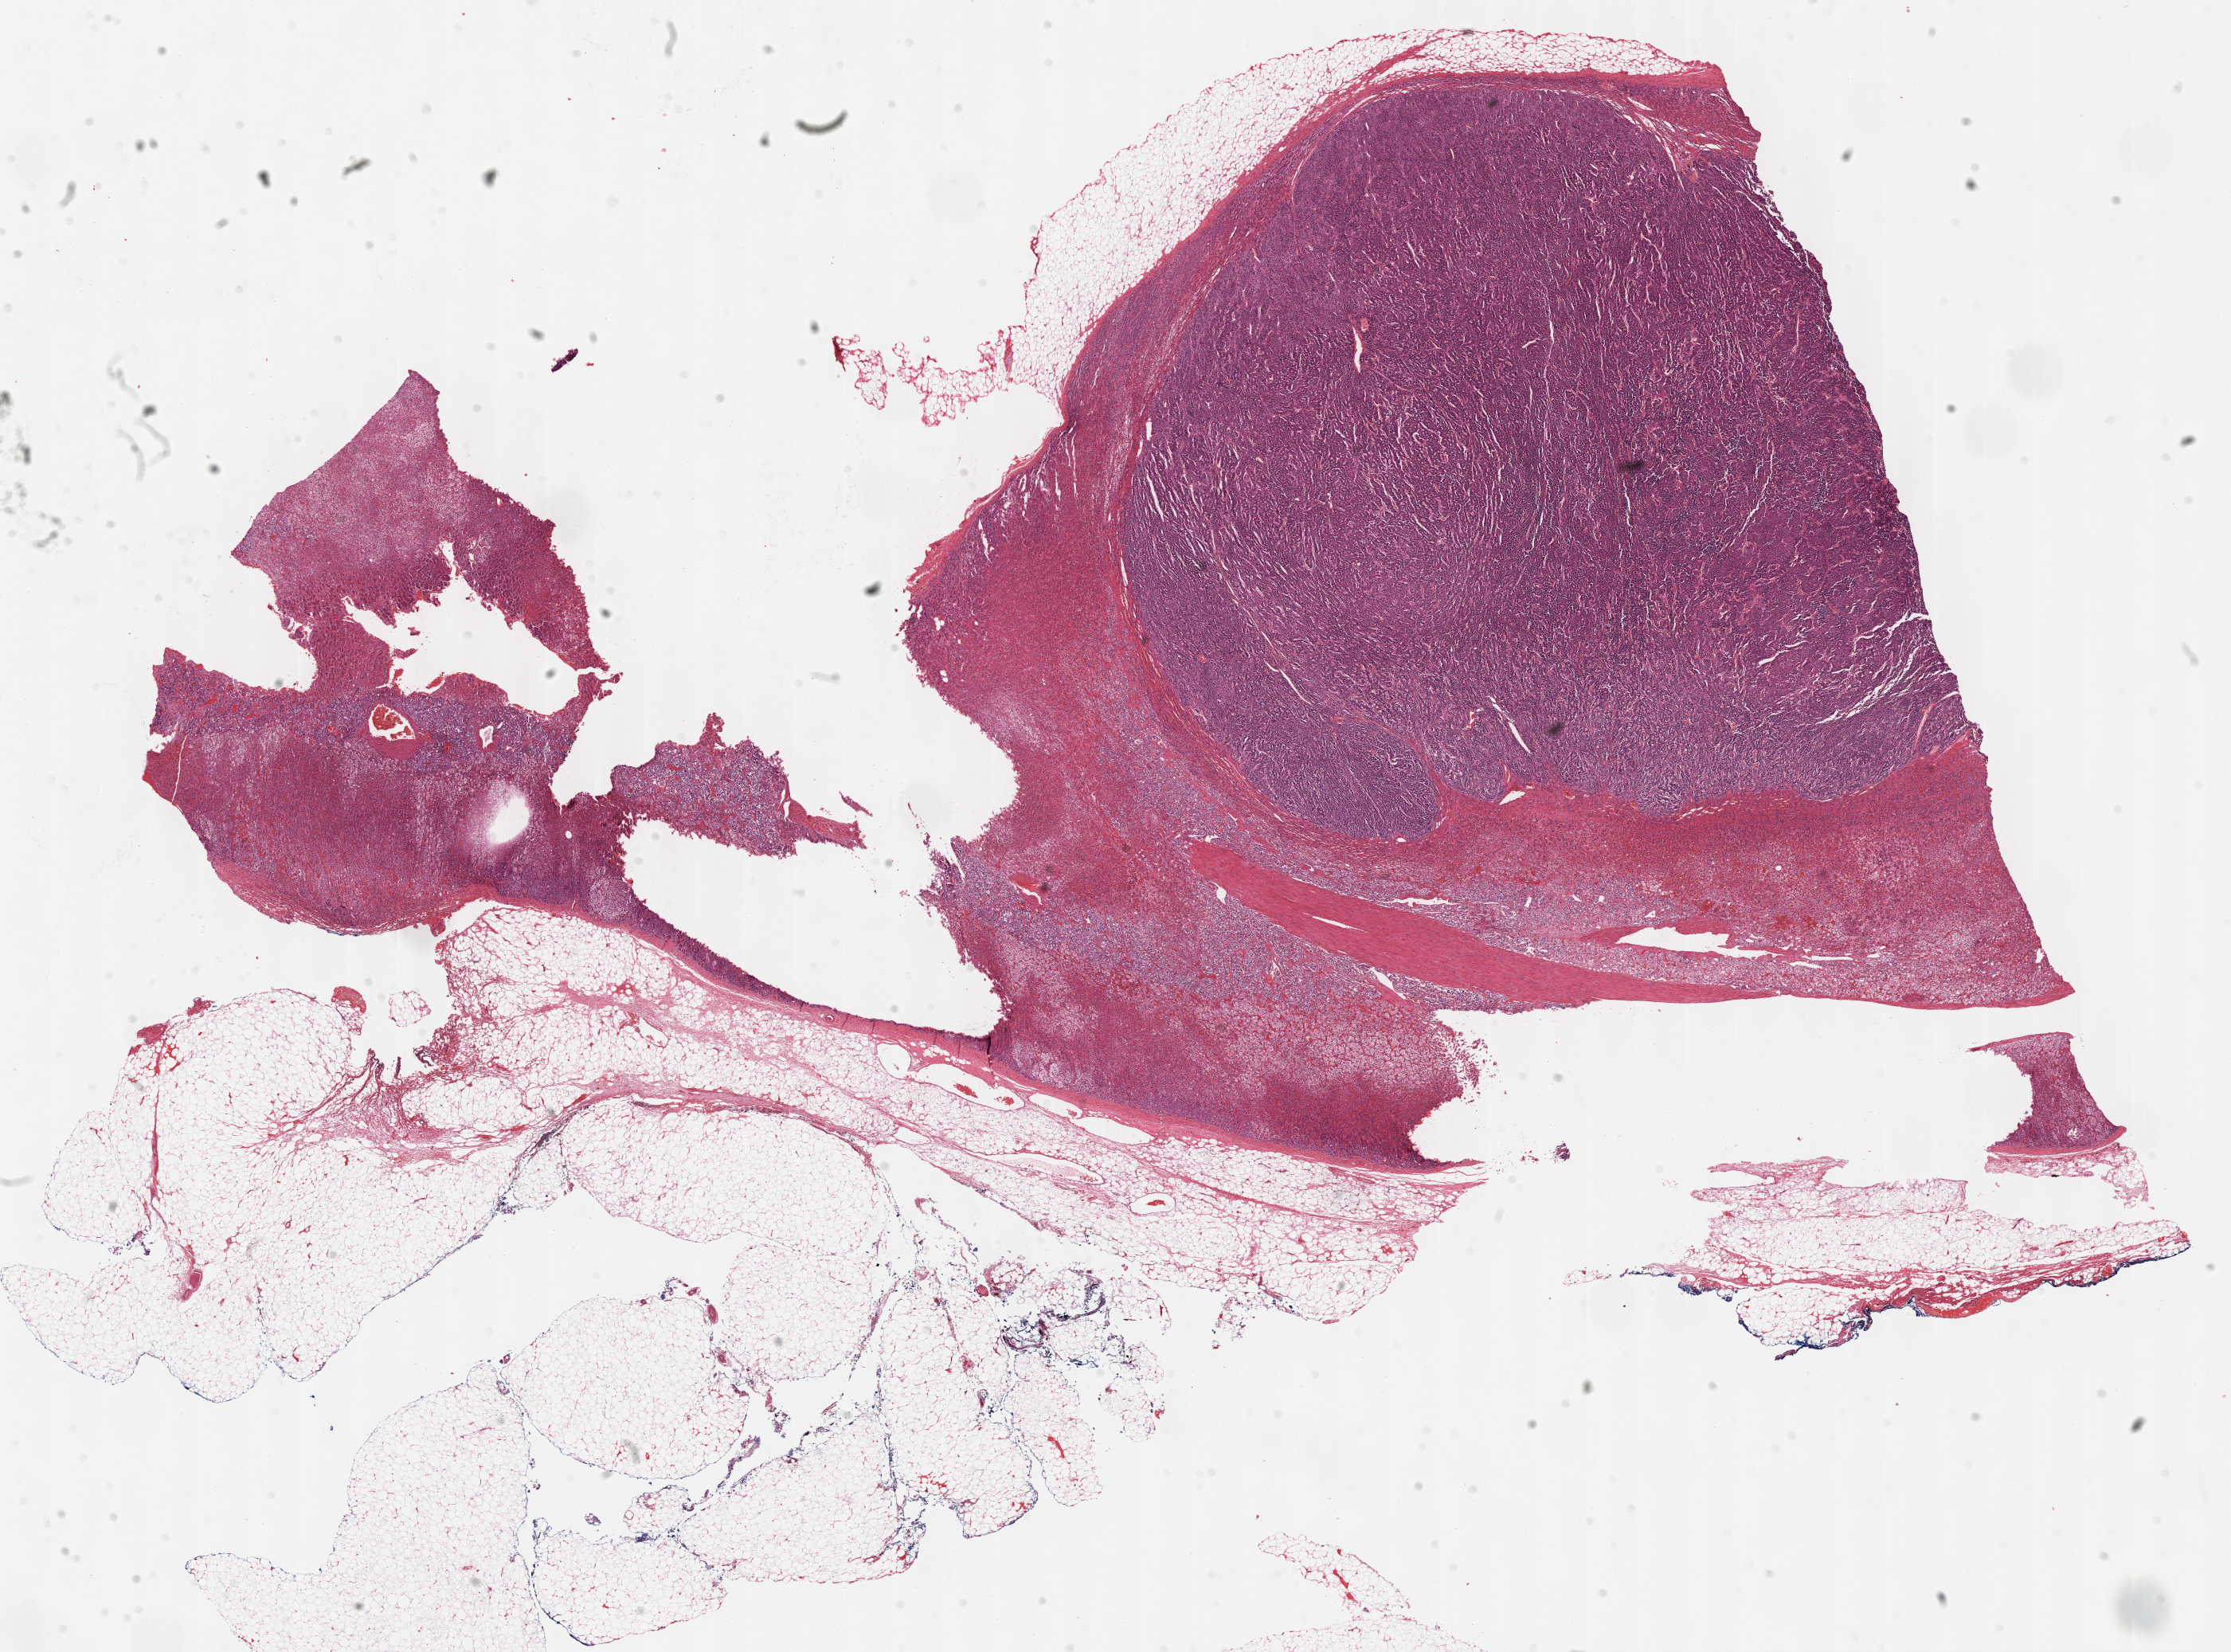
Digitized H&E tissue section (whole slide), shown as a low-resolution overview of the whole scanned area (about 22.7 x 16.8 mm). Formalin-fixed paraffin-embedded (FFPE) diagnostic section. Adrenal cortex, primary tumour sample. Male, age 58 years at initial diagnosis.
Laterality: left. Histologic diagnosis: Adrenal cortical carcinoma (cortex of adrenal gland).